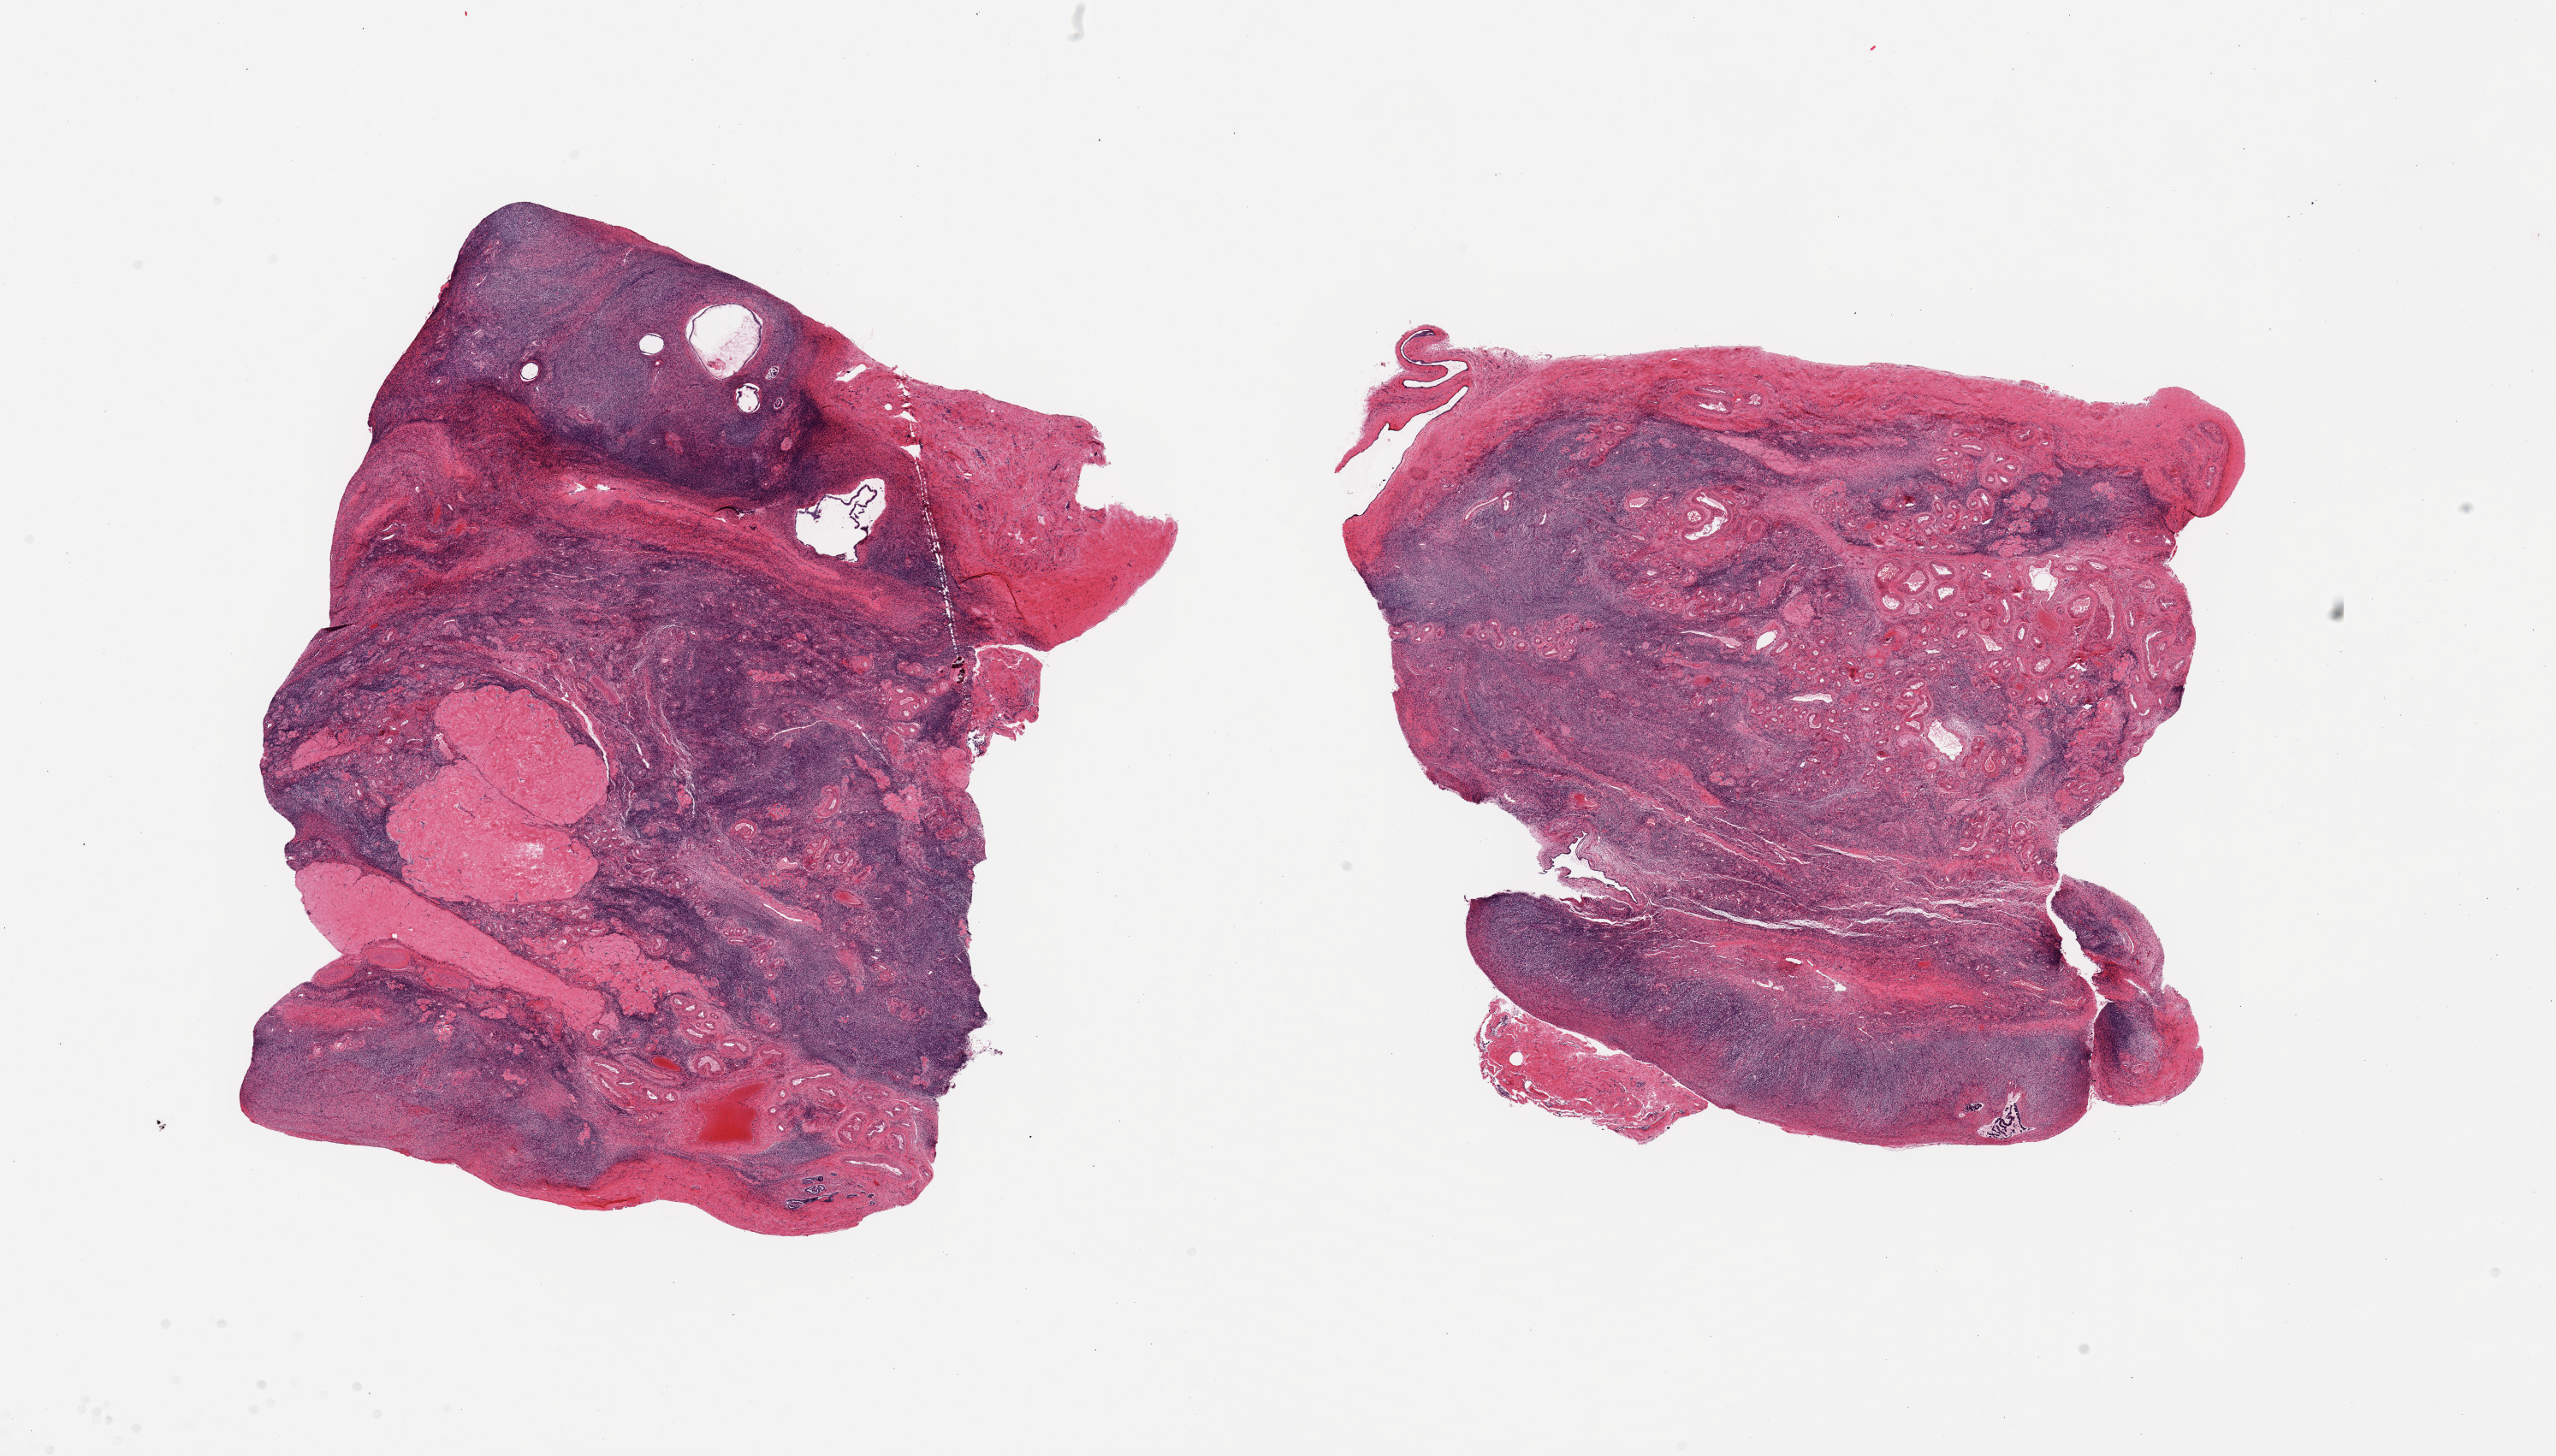
Haematoxylin and eosin whole-slide image, brightfield, a low-resolution overview of the entire scanned area, about 23.6 x 13.5 mm; PAXgene-fixed, paraffin-embedded tissue; section of ovary (target tissue); tissue donor sample.
Review note (as recorded): 2 pieces; several cystic follicles & corpora albicantia in 1 piece.